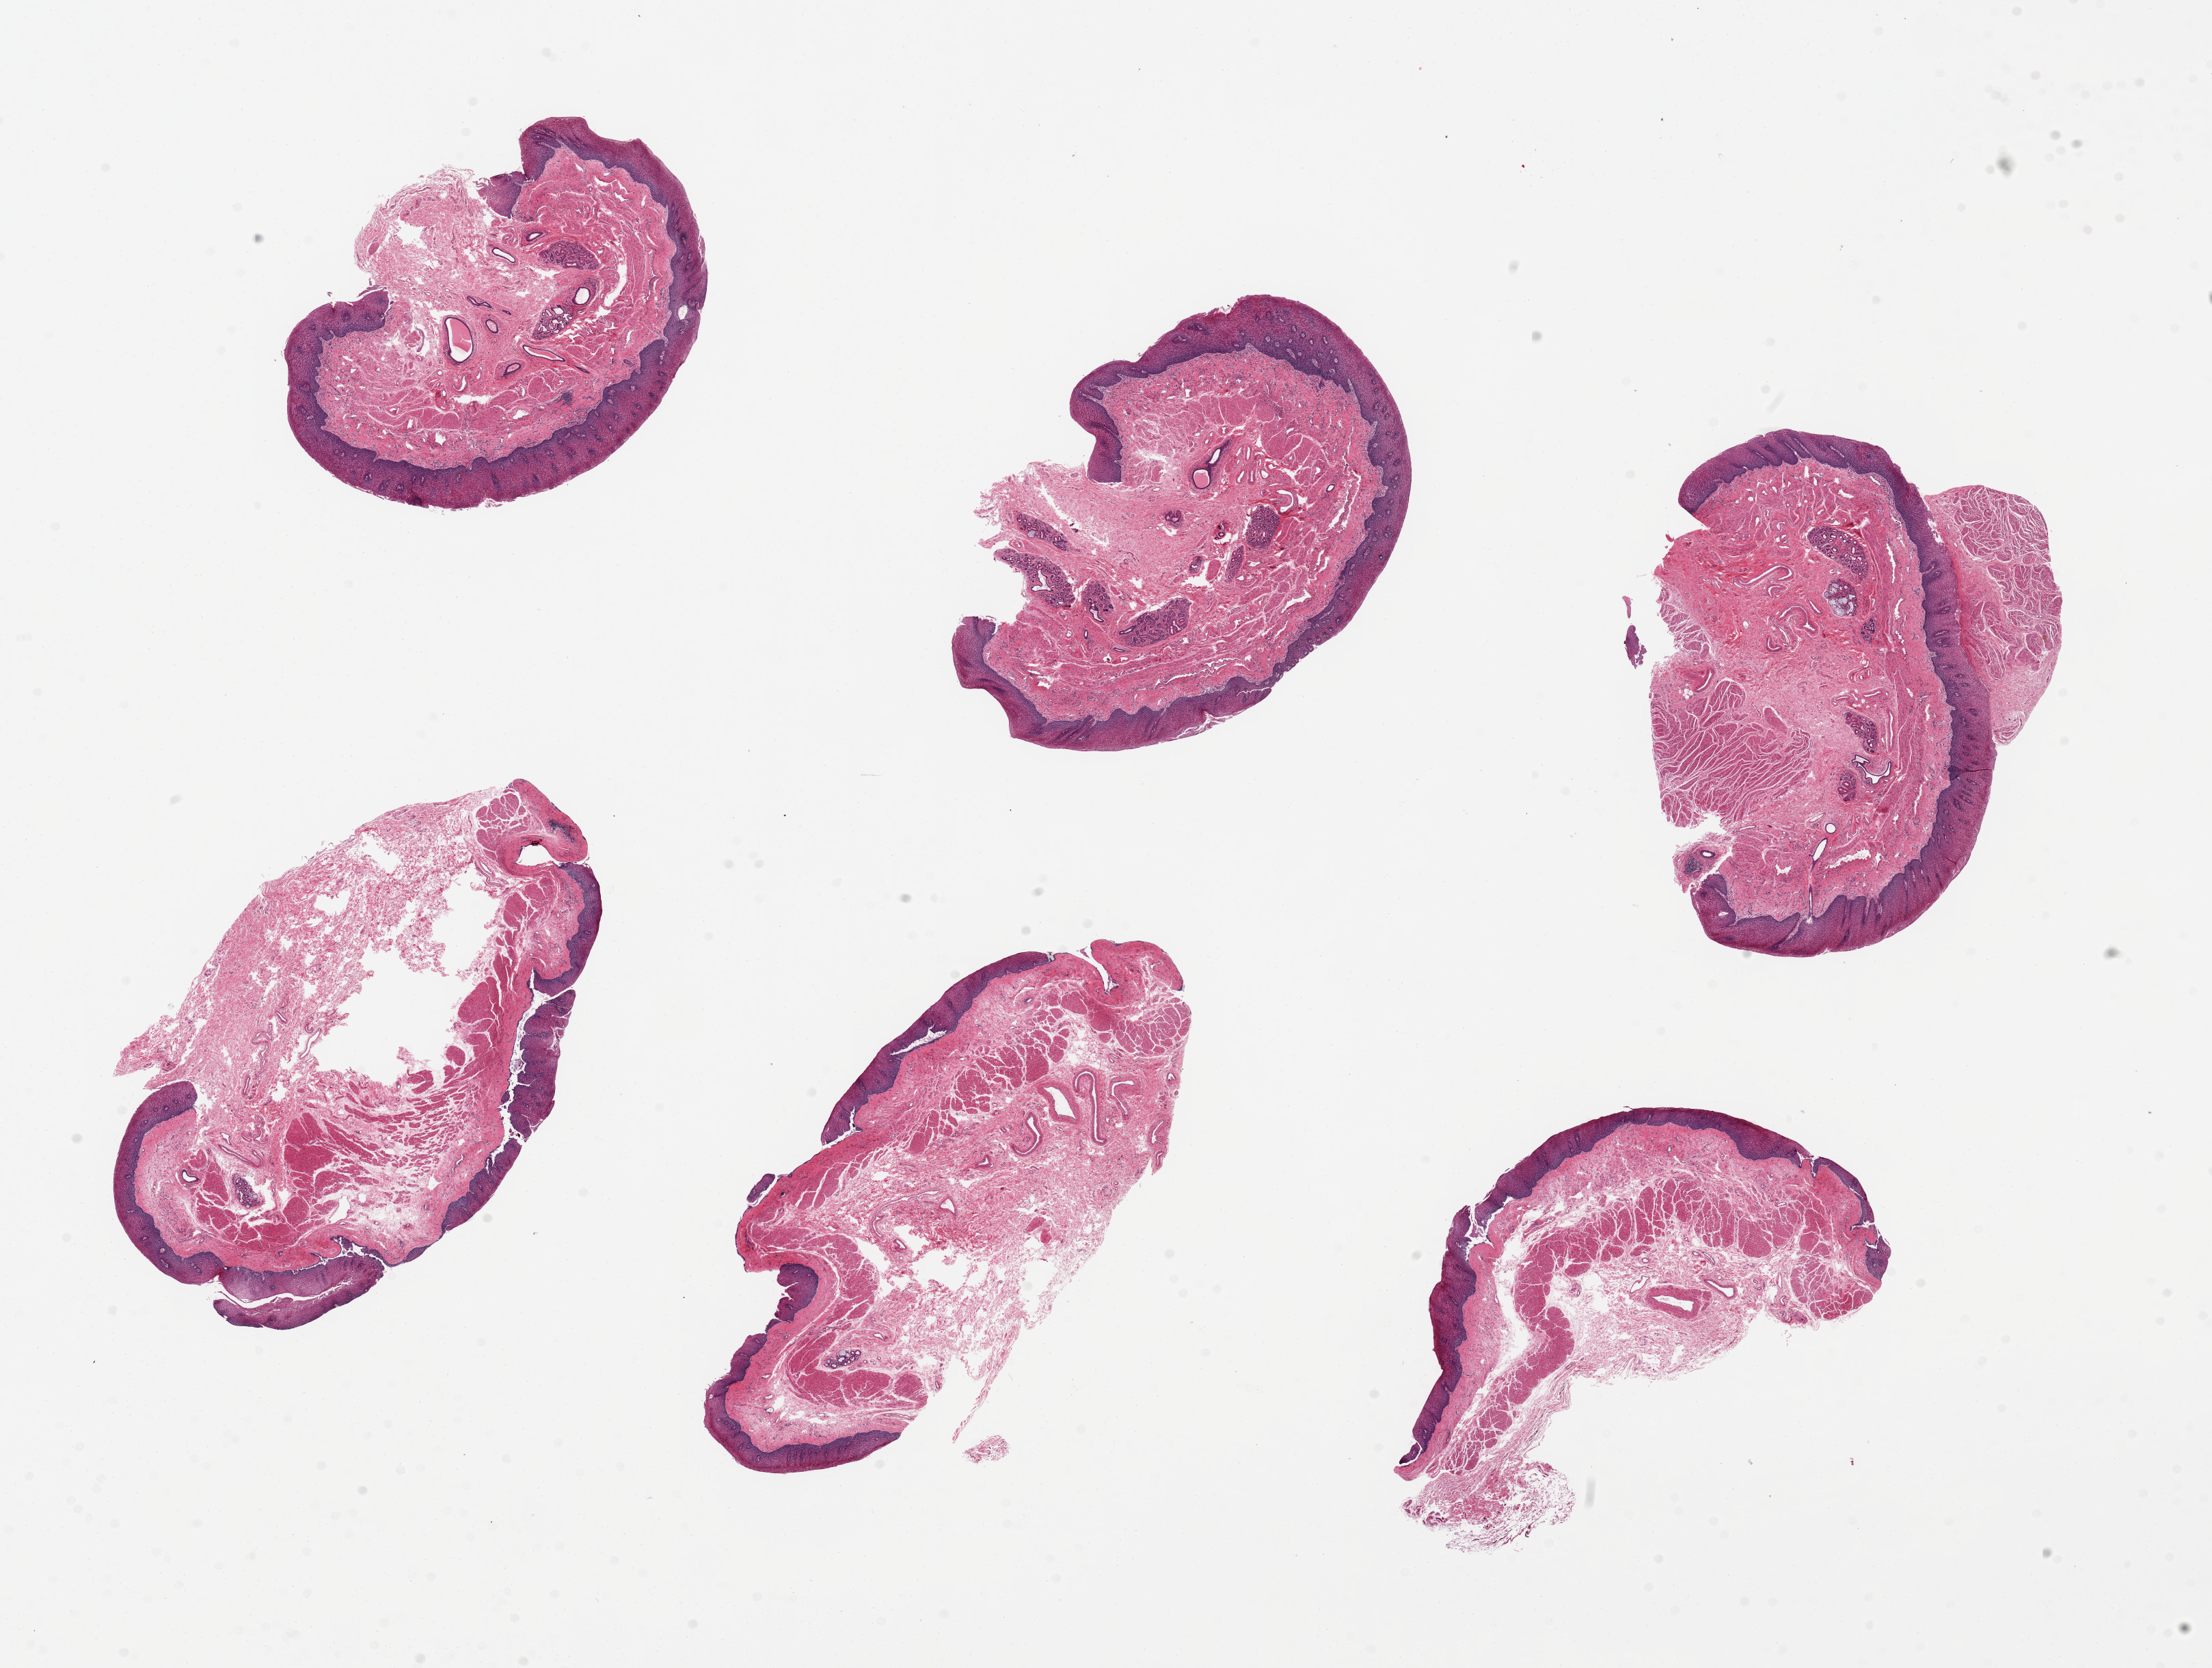
Whole-slide image, hematoxylin and eosin (H&E) stain, brightfield, a low-resolution overview of the entire scanned area, about 25.6 x 19.3 mm; PAXgene-fixed, paraffin-embedded tissue; target tissue: esophageal mucous membrane; tissue donor sample. Donor: female.
- reviewer comment on this tissue sample: 6 pieces, up to 7x4mm; squamous mucosa 10-15% thickness, submucosal glands abundant